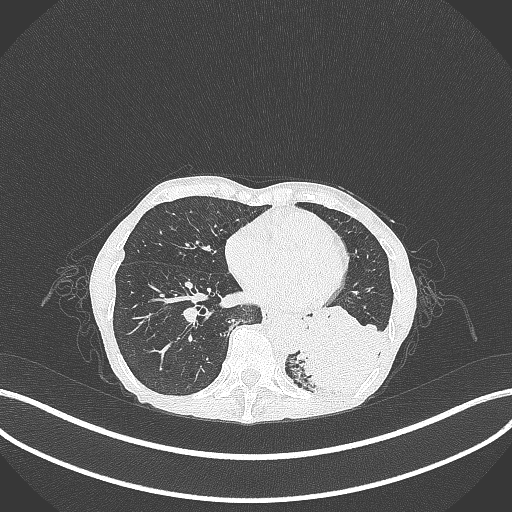
Chest CT, one axial slice; slice 92 of 347 in the series (ordered by position); lung window (W 1500 / L -600 HU); 1 mm slice thickness; 512 × 512 image matrix, field of view 400 × 400 mm. Patient: female, 70 years. Case-level facts recorded for this patient, not image findings: clinical TNM (as recorded): T3 N0 M0; histopathological grade: G3.
Structures marked on this image (rectangle marked by the reading radiologist):
- lung tumour (recorded histology: small cell carcinoma): bounding box (x1, y1, x2, y2) in pixels: (296, 311, 387, 396)